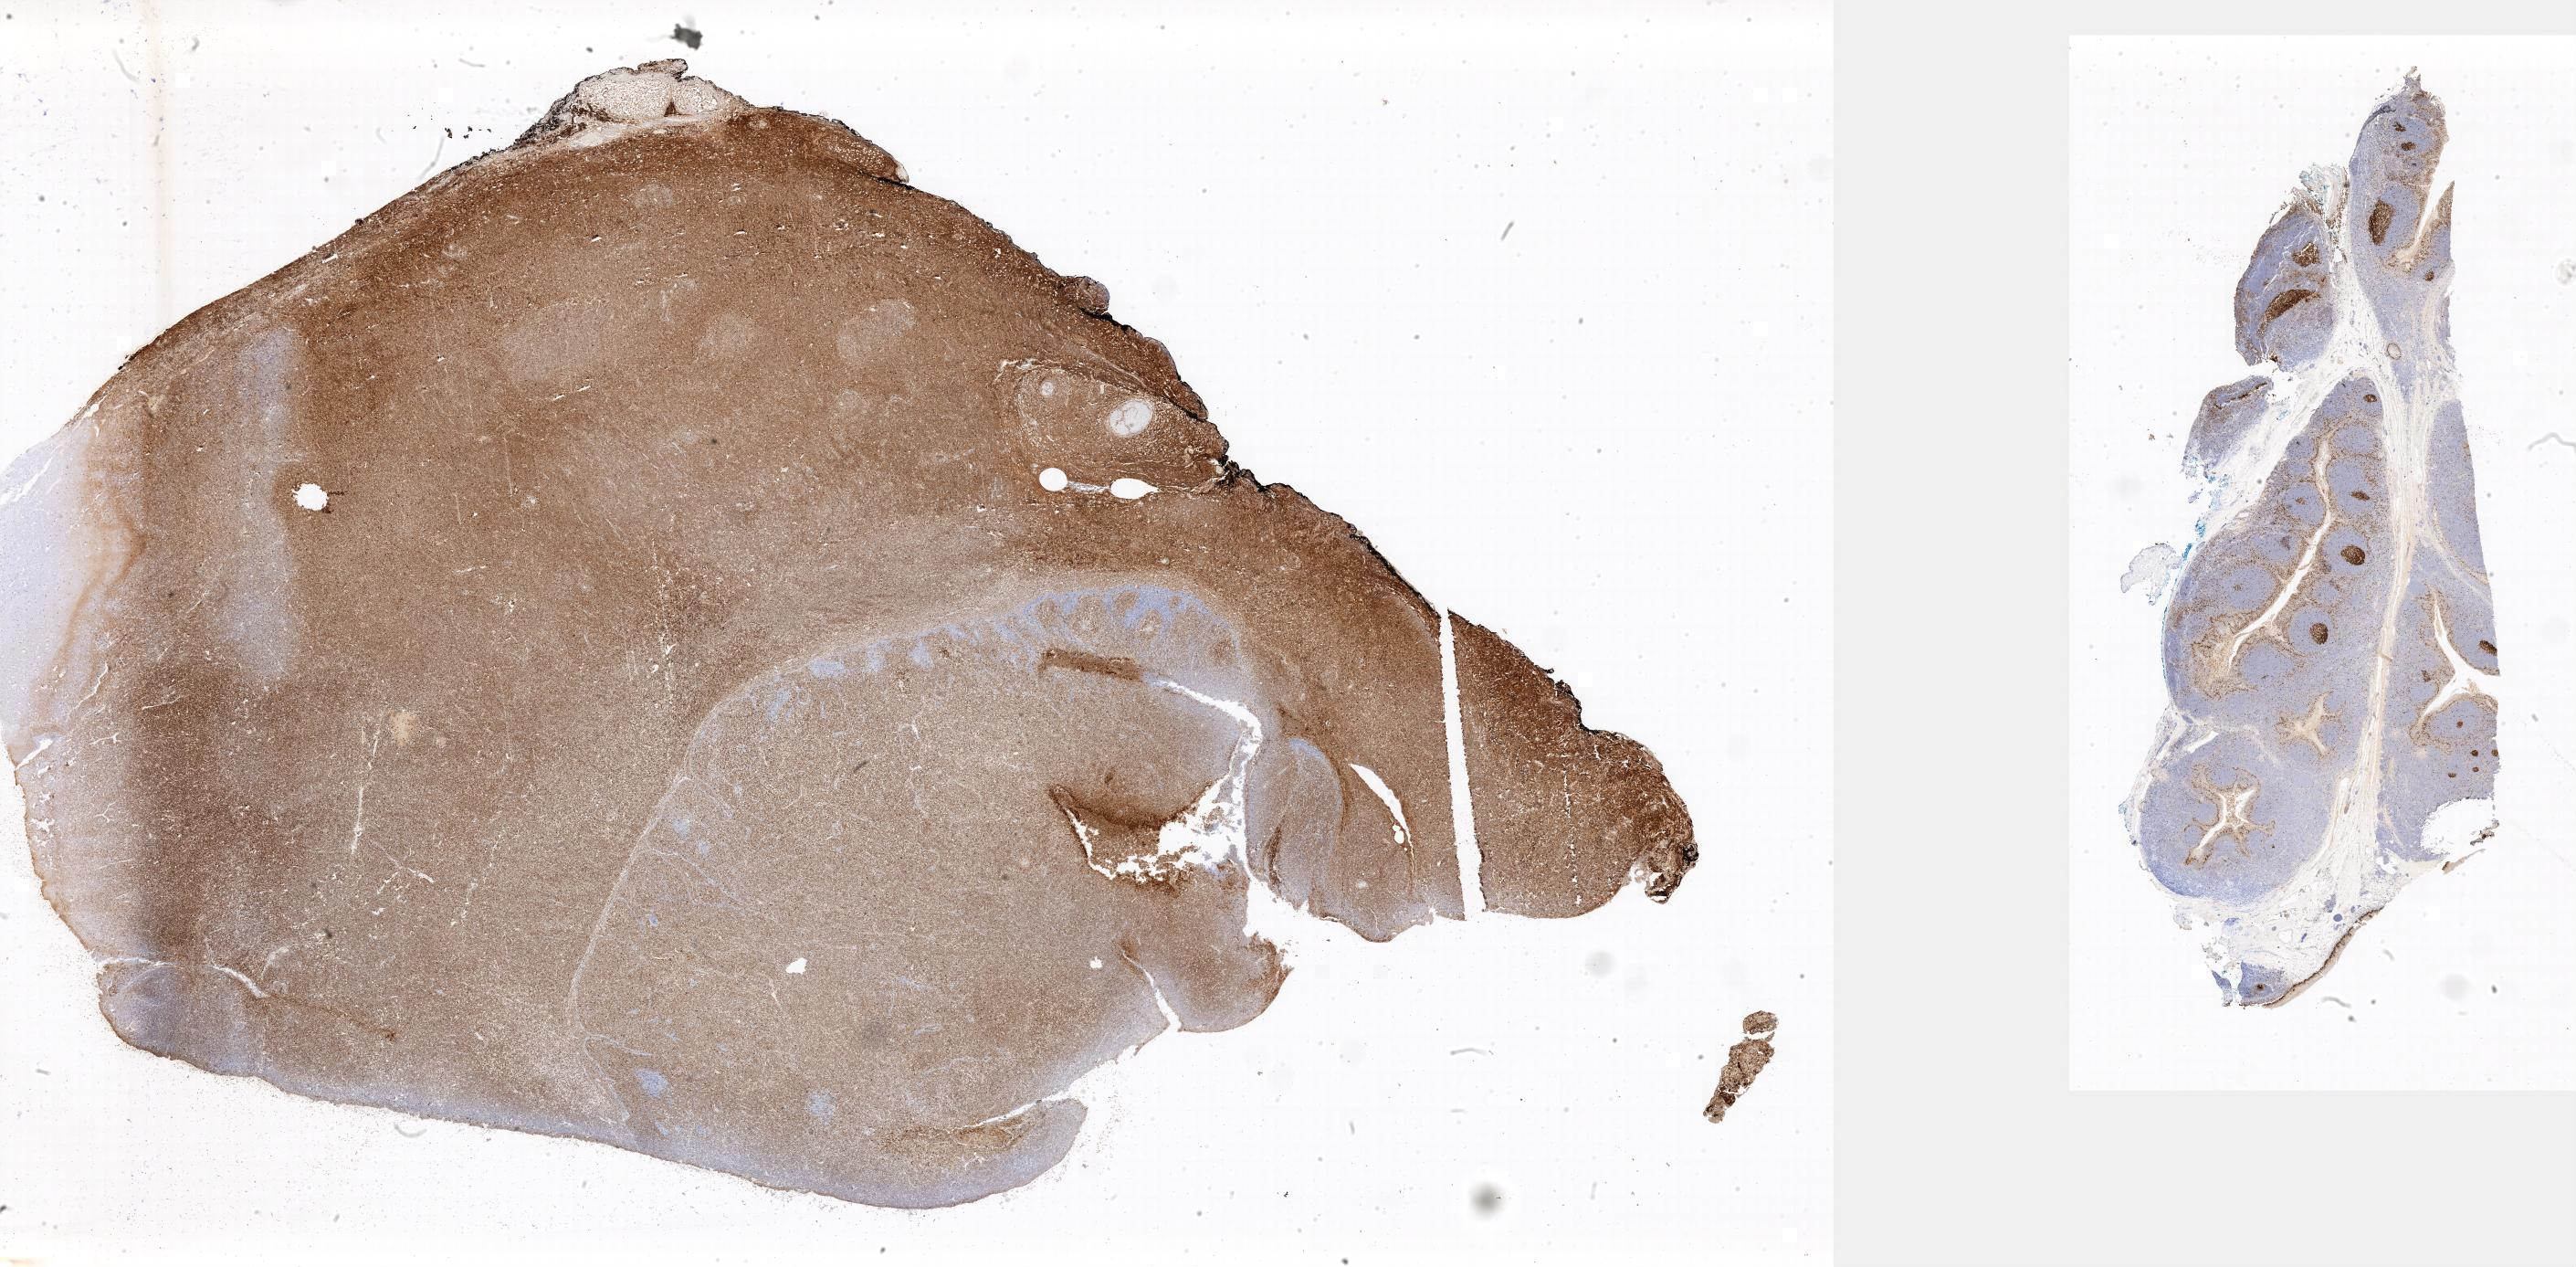
IHC for Ki-67, whole-slide image, low-resolution overview of the scanned area; specimen: tumor tissue; anatomic site: lymph node of head and neck. Male, age 6 years at initial diagnosis.
Diagnosis: Burkitt lymphoma, NOS.